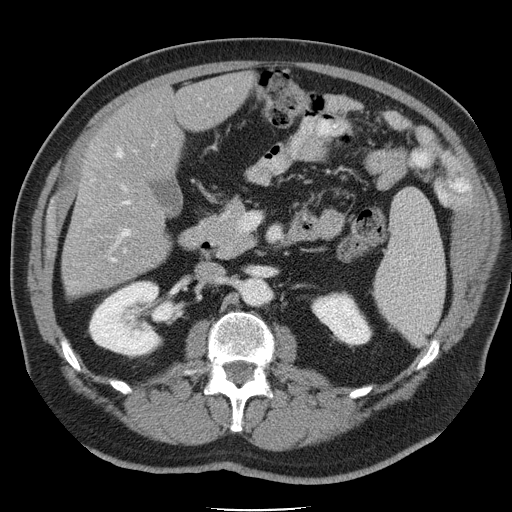
Contrast-enhanced abdominal CT, one axial slice. Position 19 of 45 along the scan axis. Intravenous contrast given. Soft-tissue window (W 400 / L 40 HU). 512 × 512 image matrix, field of view 386 × 386 mm. Male patient, age 65 years. Case-level facts recorded for this patient, not image findings: diagnosis: colorectal cancer liver metastases, imaged before liver resection; multiple liver metastases: yes; largest metastasis: 4.9 cm; disease in both lobes: no.
Outlined on this slice (manually delineated by an expert):
- hepatic veins: bounding box (x1, y1, x2, y2) in pixels: (109, 149, 123, 262)
- liver: (61, 74, 252, 296)
- planned liver remnant (the part of the liver to remain after resection): (95, 73, 252, 178)
- portal vein (with intrahepatic branches): (121, 186, 130, 237)